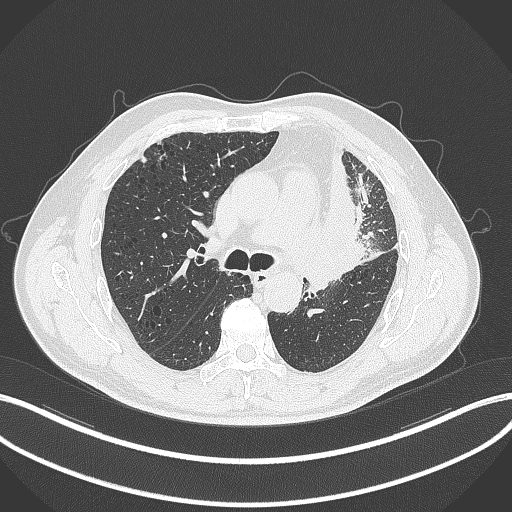
Chest CT, one axial slice. Slice 190 of 297 in the series (ordered by position). 120 kVp. Lung window (W 1500 / L -600 HU). 1 mm slice thickness. 512 × 512 image matrix, field of view 400 × 400 mm. Patient: male, 68 years. From the clinical record (not read from this slice): clinical TNM (as recorded): T3 N3 M1.
Annotated regions visible in this slice (rectangle marked by the reading radiologist):
- lung tumour (recorded histology: adenocarcinoma): bounding box (x1, y1, x2, y2) in pixels: (317, 150, 383, 282)